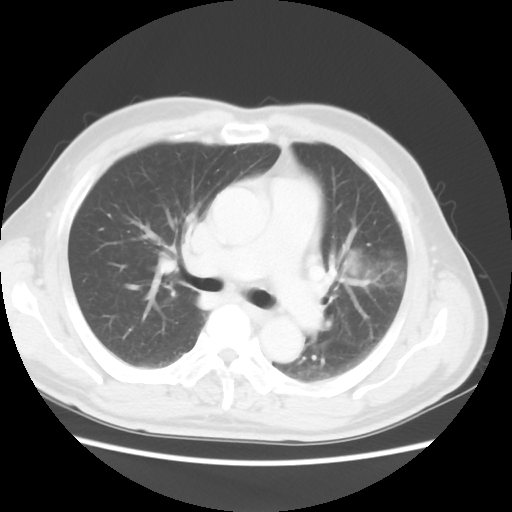
Chest CT, one axial slice; slice 30 of 50 in the series (ordered by position); reconstruction kernel STANDARD; lung window (W 1500 / L -600 HU); 512 × 512 image matrix, field of view 360 × 360 mm. Patient: male, 69 years. From the clinical record (not read from this slice): clinical TNM (as recorded): T3 N1 M1a.
Annotated regions visible in this slice (rectangle marked by the reading radiologist):
- lung tumour (recorded histology: squamous cell carcinoma): bounding box (x1, y1, x2, y2) in pixels: (342, 236, 414, 295)